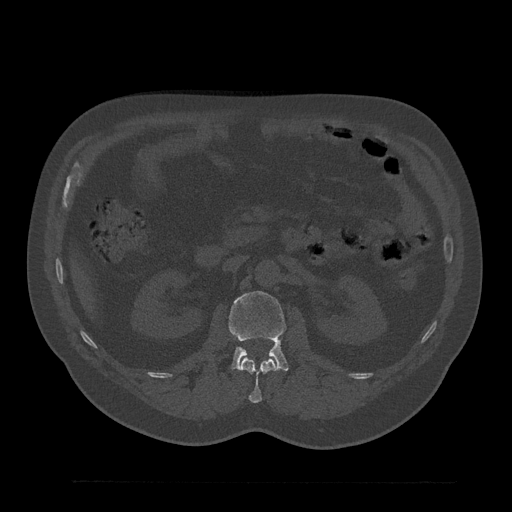
CT including the spine, one axial slice; position 127 of 797 along the scan axis; reconstruction kernel Br40s/3; 120 kVp; bone window (W 1800 / L 400 HU); 0.5 mm slice thickness; 512 × 512 image matrix, field of view 430 × 430 mm. Patient: male, 61 years. From the clinical record (not read from this slice): primary cancer: prostate.
Structures marked on this image (semi-automatic segmentation, software-assisted and operator-edited):
- L1 vertebra: bounding box <239,358,279,403> (left, top, right, bottom; pixels)
- L2 vertebra: <229,291,288,370>